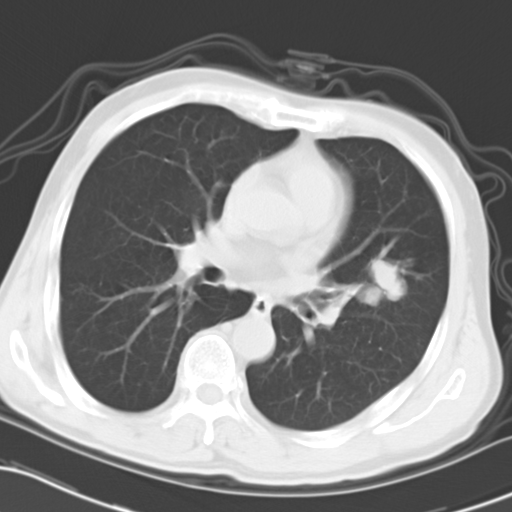
Chest CT, one axial slice; position 14 of 27 along the scan axis; lung window (W 1500 / L -600 HU); 10 mm slice thickness; 512 × 512 image matrix. Patient: male, 60 years. Case-level facts recorded for this patient, not image findings: clinical TNM (as recorded): T1c N1 M0; histopathological grade: G3.
Outlined on this slice (rectangle marked by the reading radiologist):
- lung tumour (recorded histology: adenocarcinoma): bounding box <366,253,405,298> (left, top, right, bottom; pixels)
- lung tumour (recorded histology: adenocarcinoma): <370,255,402,301>